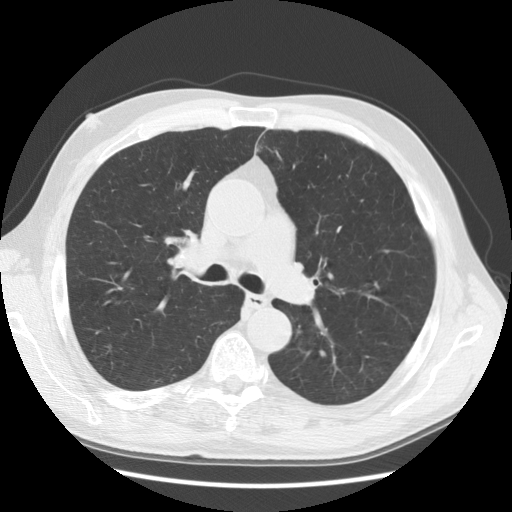
Axial slice from a low-dose chest CT screening exam. First (baseline) screen. Lung window (W 1500 / L -600 HU). Standard (soft-tissue) reconstruction kernel (STANDARD). Slice 57 of 145 in the series. Male, age 60 years at enrolment. Current smoker at enrolment.
• Expert reader's lesion annotation, box from (x=154, y=227) to (x=214, y=284) px.
• No non-calcified nodule or mass ≥4 mm was recorded by the screening reader at this exam.
• Lung cancer was diagnosed 193 days after this screen: squamous cell carcinoma, NOS, right upper lobe, moderately differentiated (G2), stage IIIB (AJCC 6th edition), 52 mm at pathology.